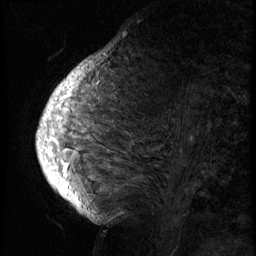
Breast MRI (dynamic contrast-enhanced), one sagittal slice. Position 29 of 74 along the scan axis. 3 images stored at this slice position (order not interpretable as contrast timing). 1.5 T. TE 4.2 ms, TR 8.9 ms. 2.5 mm slice thickness. 256 × 256 image matrix, field of view 200 × 200 mm. Female patient, age 57 years. Case-level facts recorded for this patient, not image findings: setting: breast cancer imaged before/during neoadjuvant chemotherapy; receptor status: HER2-positive.
Annotated regions visible in this slice (semi-automatic segmentation, software-assisted and operator-edited):
- analysis volume of interest (the breast-tissue region the enhancement analysis was run in; not a lesion): box from (x=40, y=62) to (x=234, y=175) px
- tumour enhancement mask (voxels above the 140 % enhancement threshold inside the analysis volume of interest): (x=48, y=62)–(x=93, y=175)